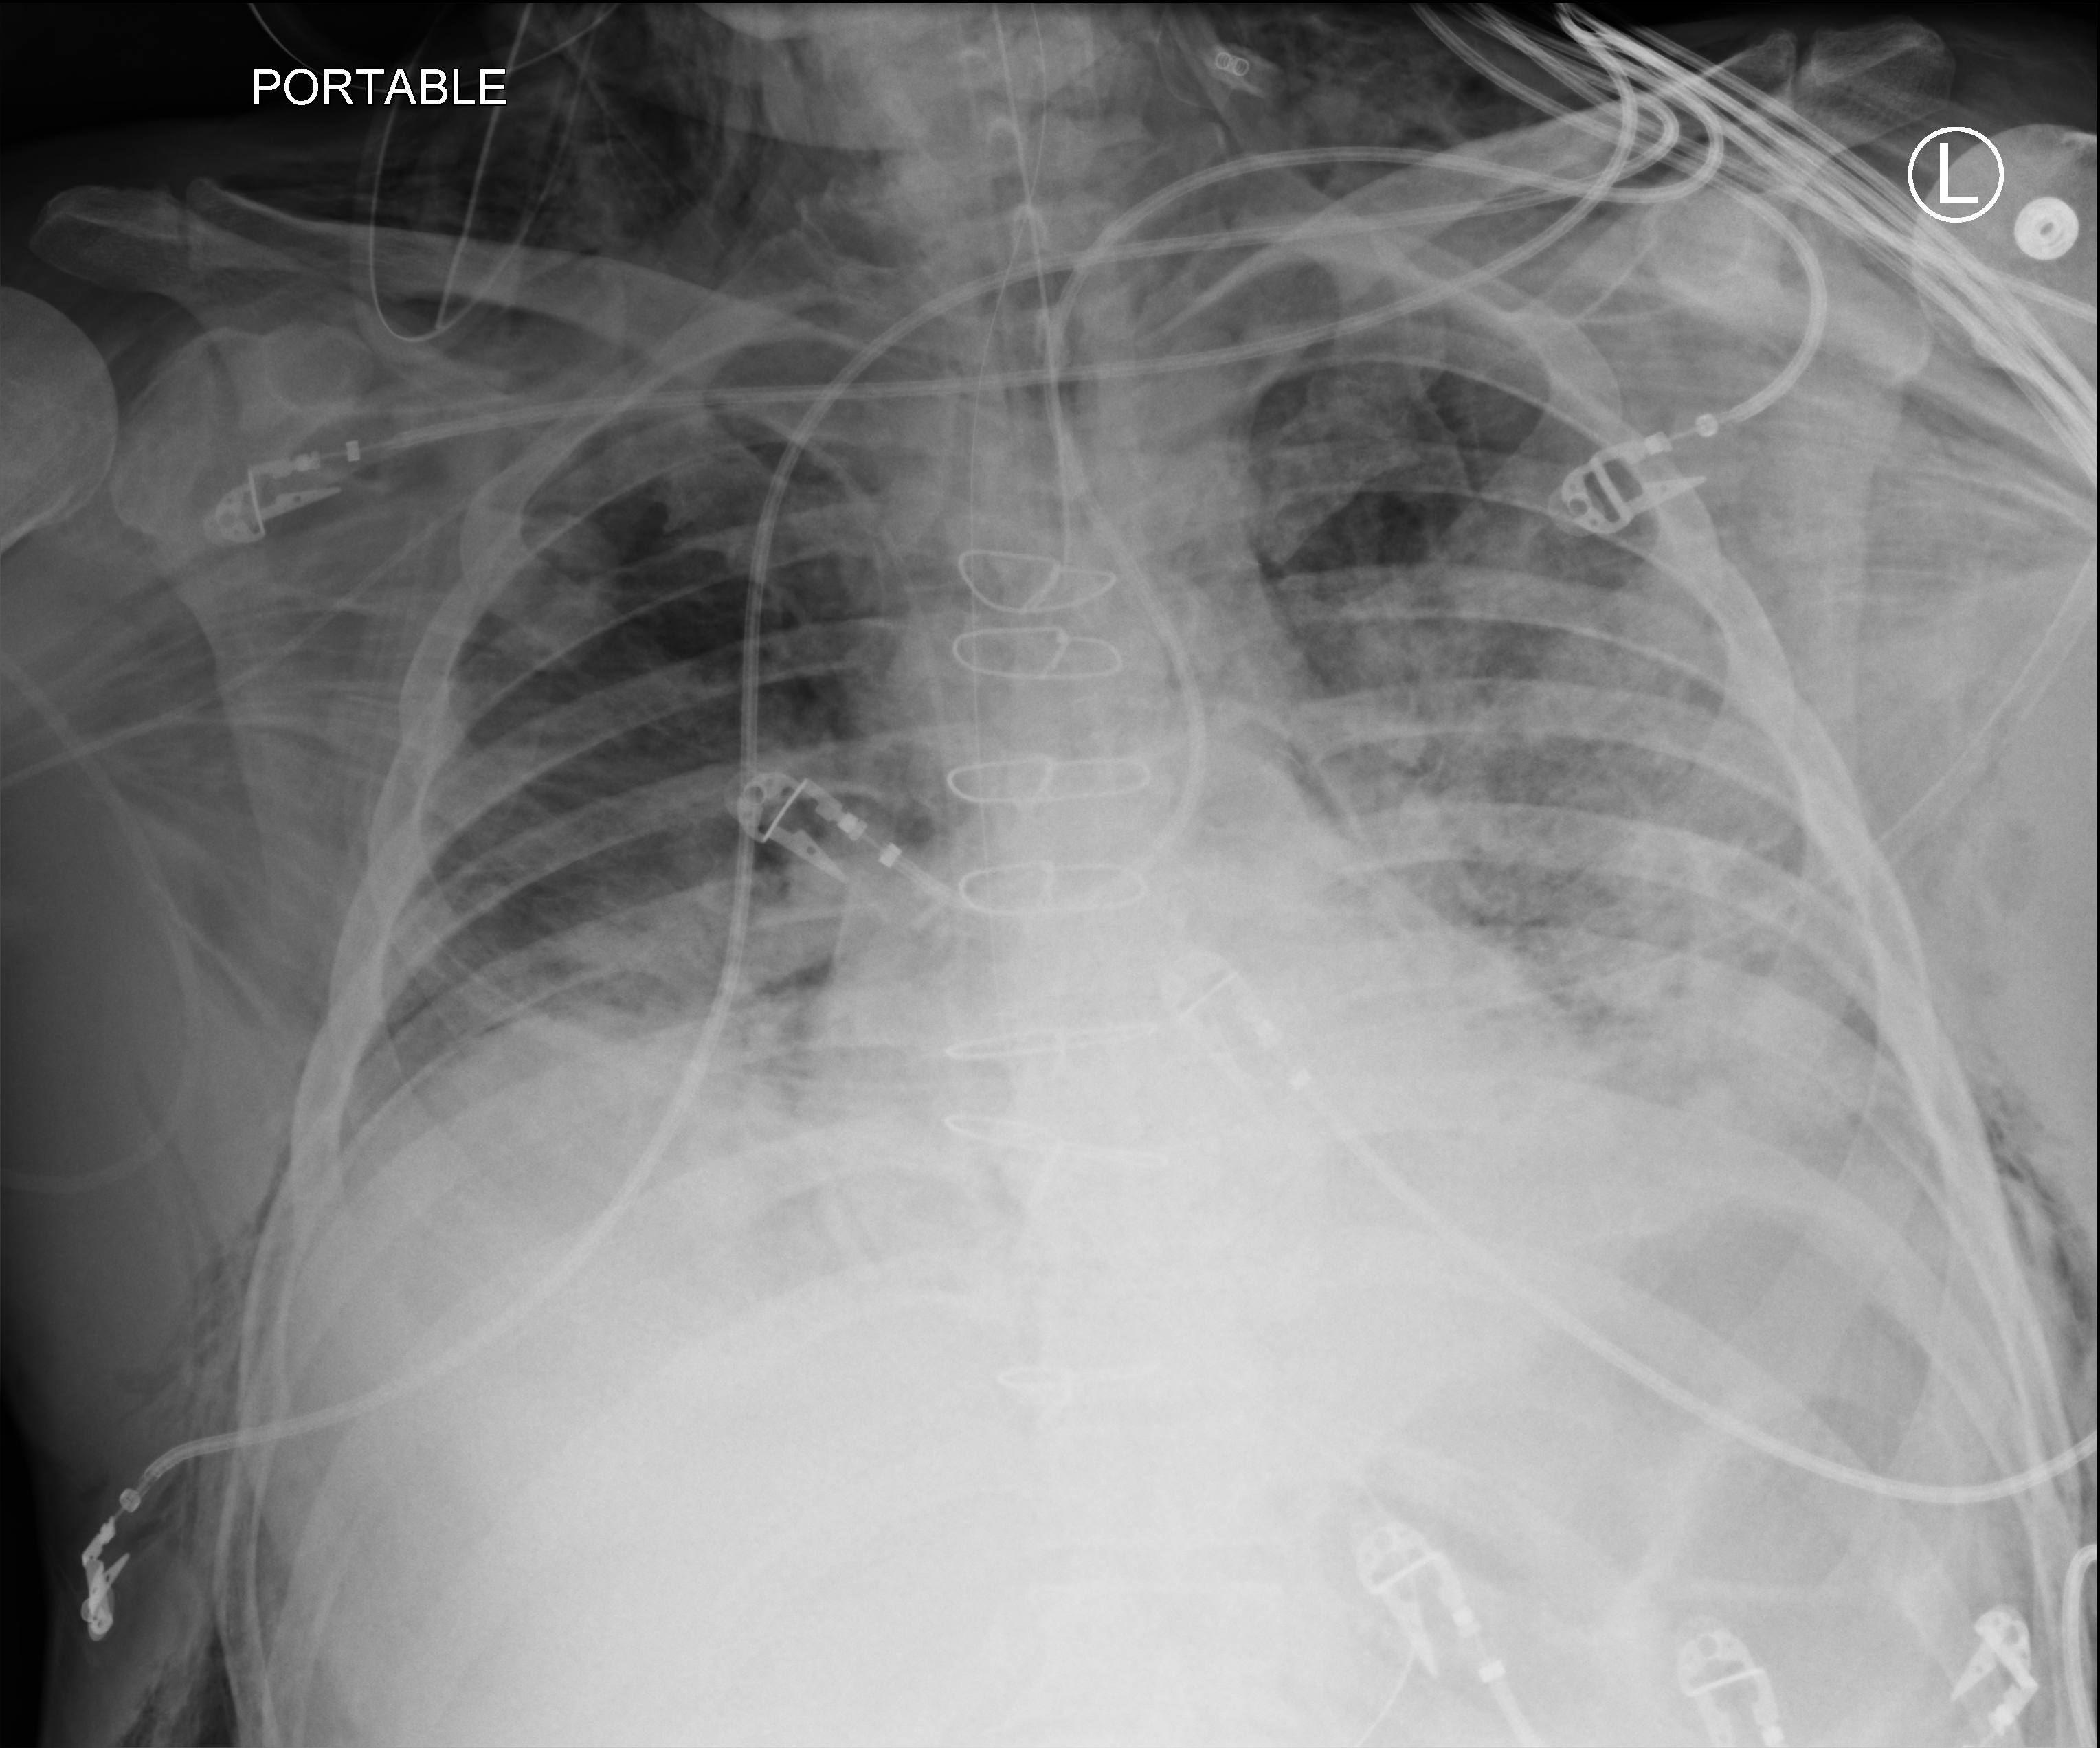
Portable chest radiograph. Male patient hospitalised with COVID-19, age 60–74 years.
Hospital-stay facts (about this admission, not read from this image; timing relative to this image not recorded):
- diabetes (admission record): yes
- length of hospital stay: 44 days